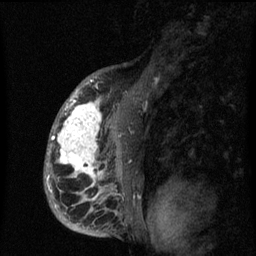
Breast MRI (dynamic contrast-enhanced), one sagittal slice. Slice 43 of 60 in the series (ordered by position). Dynamic contrast-enhanced series, image 2 of 3 at this slice position (ordered by acquisition). 1.5 T. TE 4.2 ms, TR 8 ms. 256 × 256 image matrix, field of view 190 × 190 mm. Female patient, age 50 years.
Outlined on this slice (semi-automatic segmentation, software-assisted and operator-edited):
- analysis volume of interest (the breast-tissue region the enhancement analysis was run in; not a lesion): bounding box (x1, y1, x2, y2) in pixels: (44, 90, 142, 216)
- tumour enhancement mask (voxels above the 70 % enhancement threshold inside the analysis volume of interest): (47, 90, 120, 200)